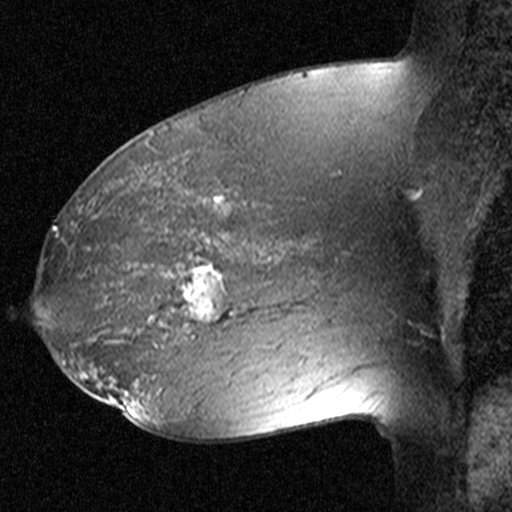
Breast MRI (dynamic contrast-enhanced), one sagittal slice. Slice 27 of 44 in the series (ordered by position). Dynamic contrast-enhanced study with each time point stored as its own series, time point 2 of 3 at this slice position (early post-contrast, ordered by acquisition time). 1.5 T. TE 4.5 ms, TR 11 ms. 512 × 512 image matrix. Female patient, age 38 years. Case-level facts recorded for this patient, not image findings: setting: breast cancer imaged before/during neoadjuvant chemotherapy; receptor status: HR-positive, HER2-negative.
Outlined on this slice (semi-automatic segmentation, software-assisted and operator-edited):
- analysis volume of interest (the breast-tissue region the enhancement analysis was run in; not a lesion): bounding box (x1, y1, x2, y2) in pixels: (152, 236, 253, 335)
- tumour enhancement mask (voxels above the 90 % enhancement threshold inside the analysis volume of interest): (169, 258, 231, 321)